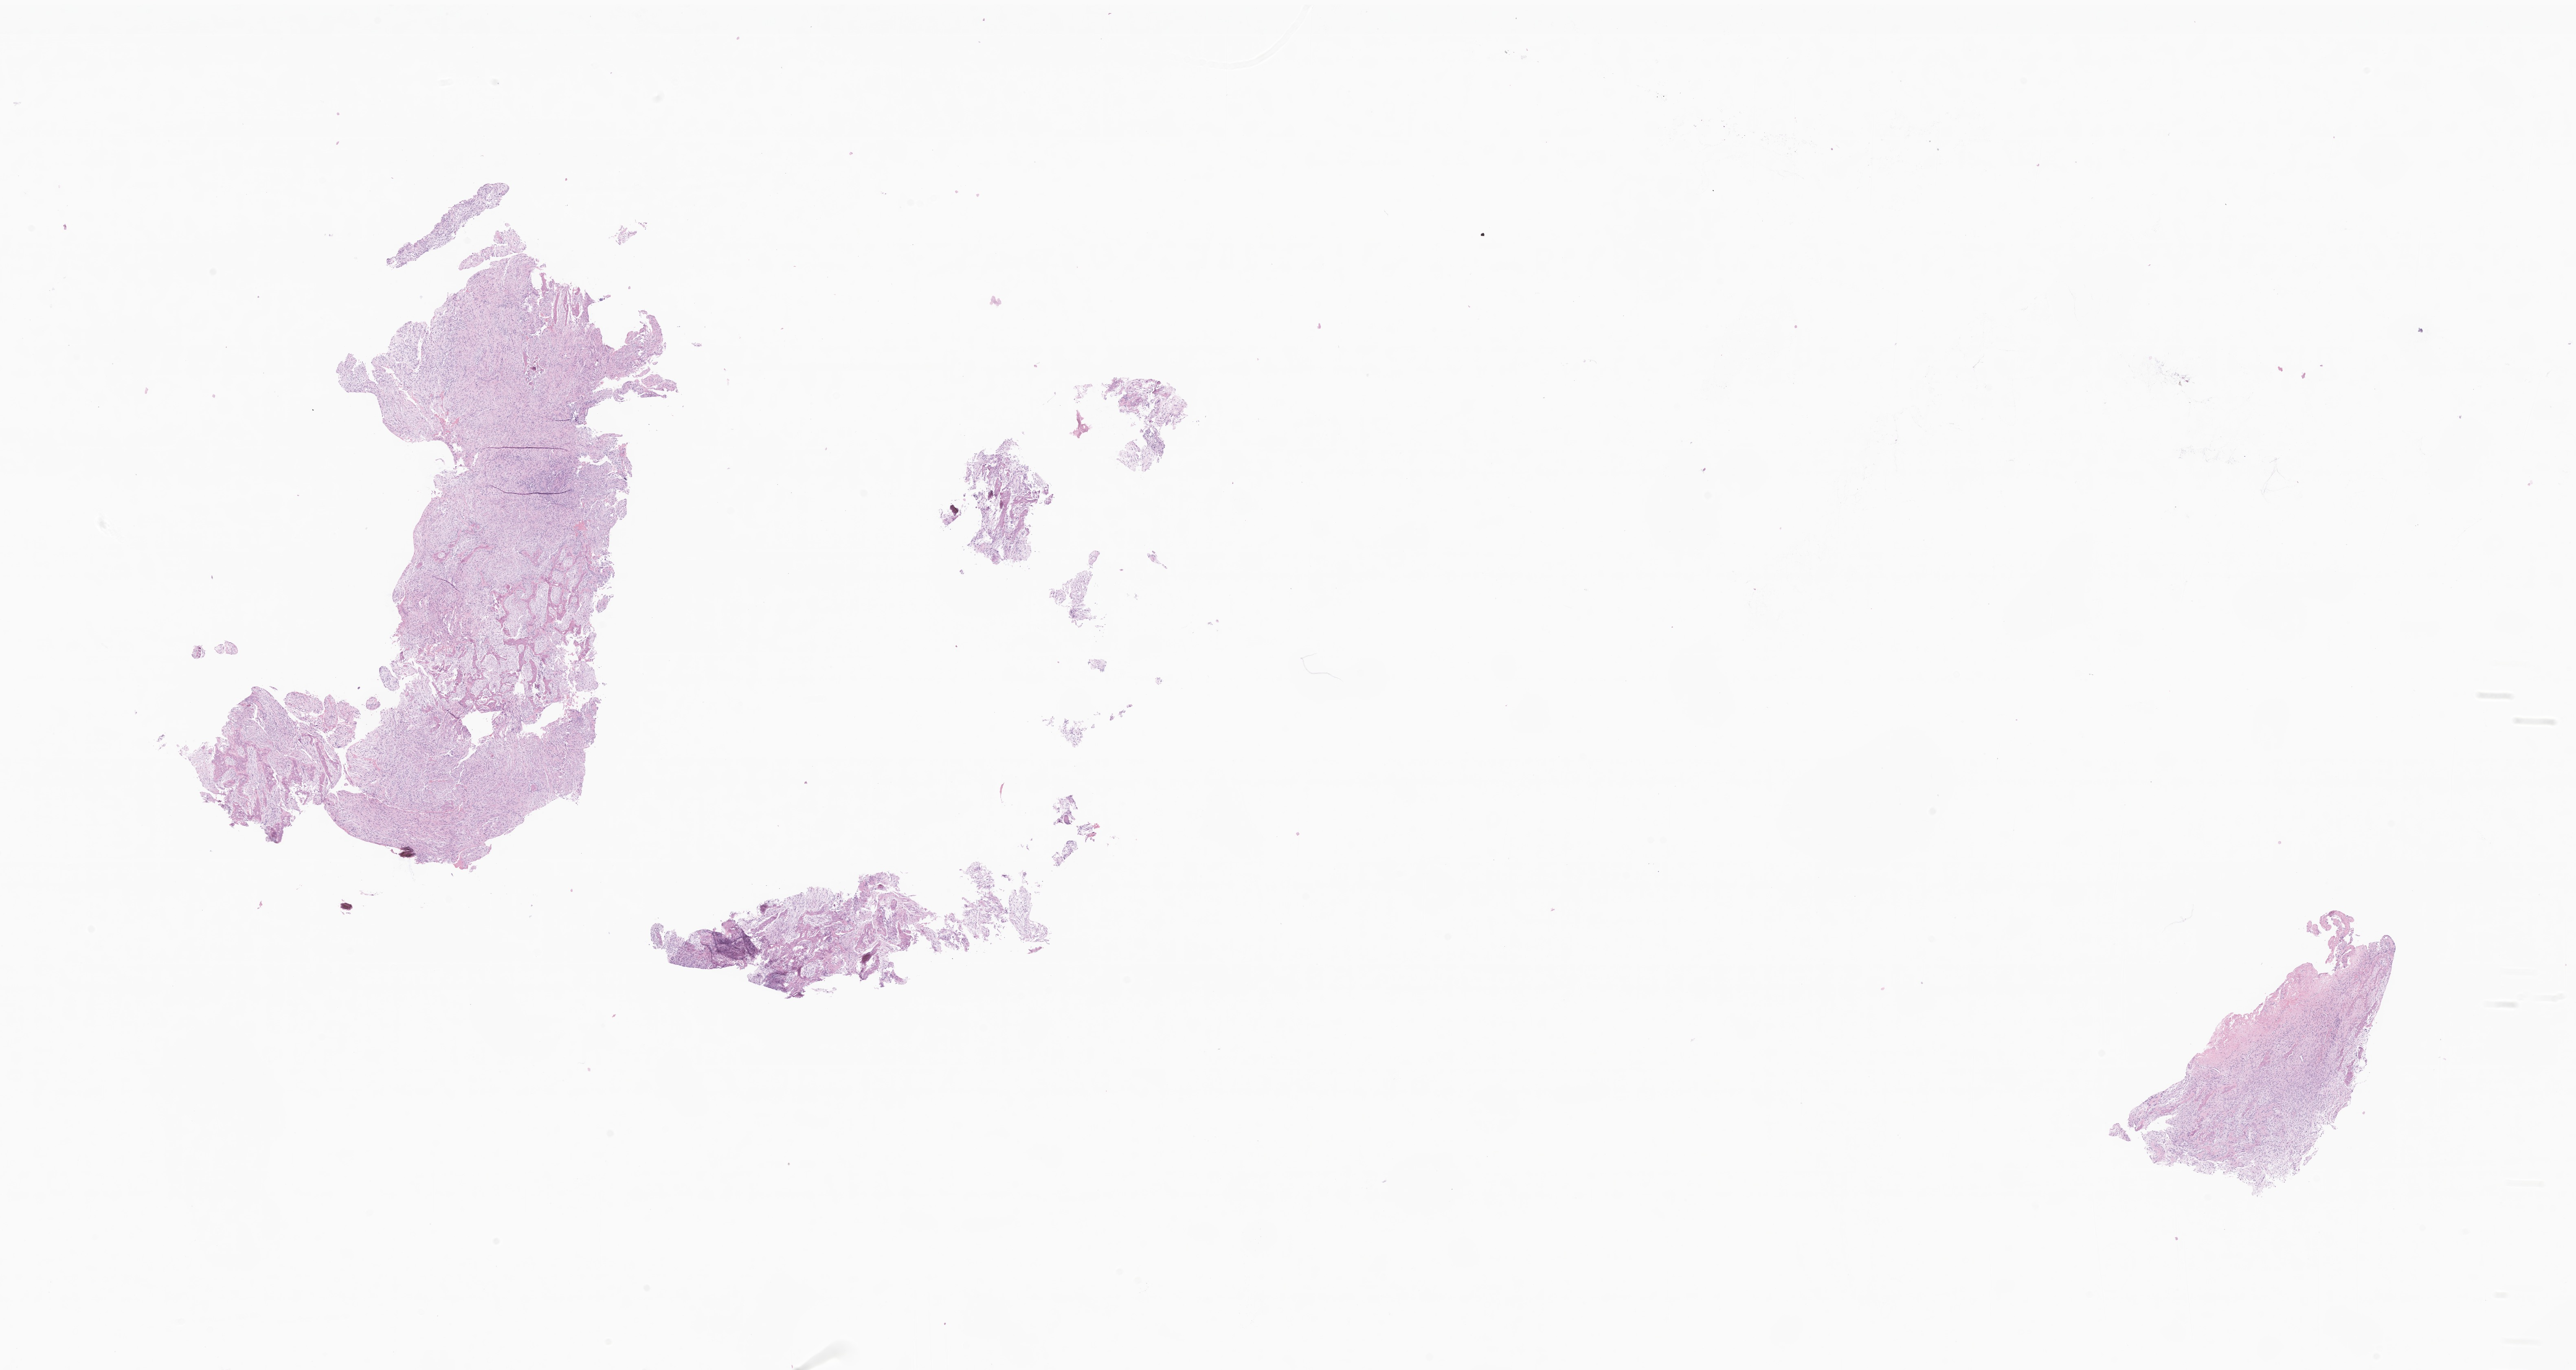
Haematoxylin and eosin whole-slide image of tumor tissue from the mandible, a low-resolution overview of the entire scanned area, about 26.7 x 14.2 mm, formalin-fixed, paraffin-embedded (FFPE) tissue. Patient female; age 91 months.
* recorded diagnosis: Spindle cell rhabdomyosarcoma